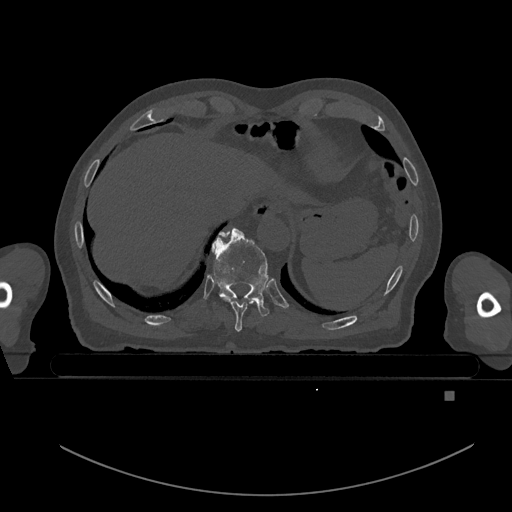
CT including the spine, one axial slice. Position 113 of 969 along the scan axis. Bone window (W 1800 / L 400 HU). 0.5 mm slice thickness. 512 × 512 image matrix, field of view 456 × 456 mm. Male patient, age 82 years. Case-level facts recorded for this patient, not image findings: primary cancer: prostate; vertebrae with lytic lesions (as recorded): T11, T9, T8, T2.
Outlined on this slice (semi-automatically segmented with operator editing):
- T10 vertebra: bounding box [x1, y1, x2, y2] px = [211, 227, 269, 316]
- T9 vertebra: [219, 232, 254, 332]